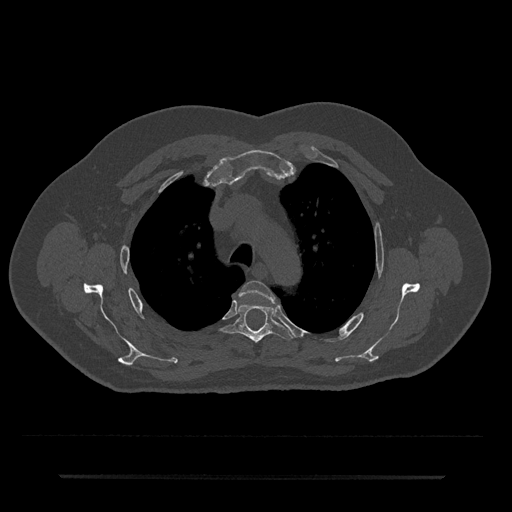
CT including the spine, one axial slice. Position 537 of 797 along the scan axis. Reconstruction kernel Br40s/3. 120 kVp. Bone window (W 1800 / L 400 HU). 0.5 mm slice thickness. 512 × 512 image matrix, field of view 437 × 437 mm. Patient: male, 69 years. Case-level facts recorded for this patient, not image findings: primary cancer: prostate.
Outlined on this slice (semi-automatically segmented with operator editing):
- T3 vertebra: bounding box [x1, y1, x2, y2] px = [239, 280, 275, 303]
- T4 vertebra: [220, 304, 293, 343]